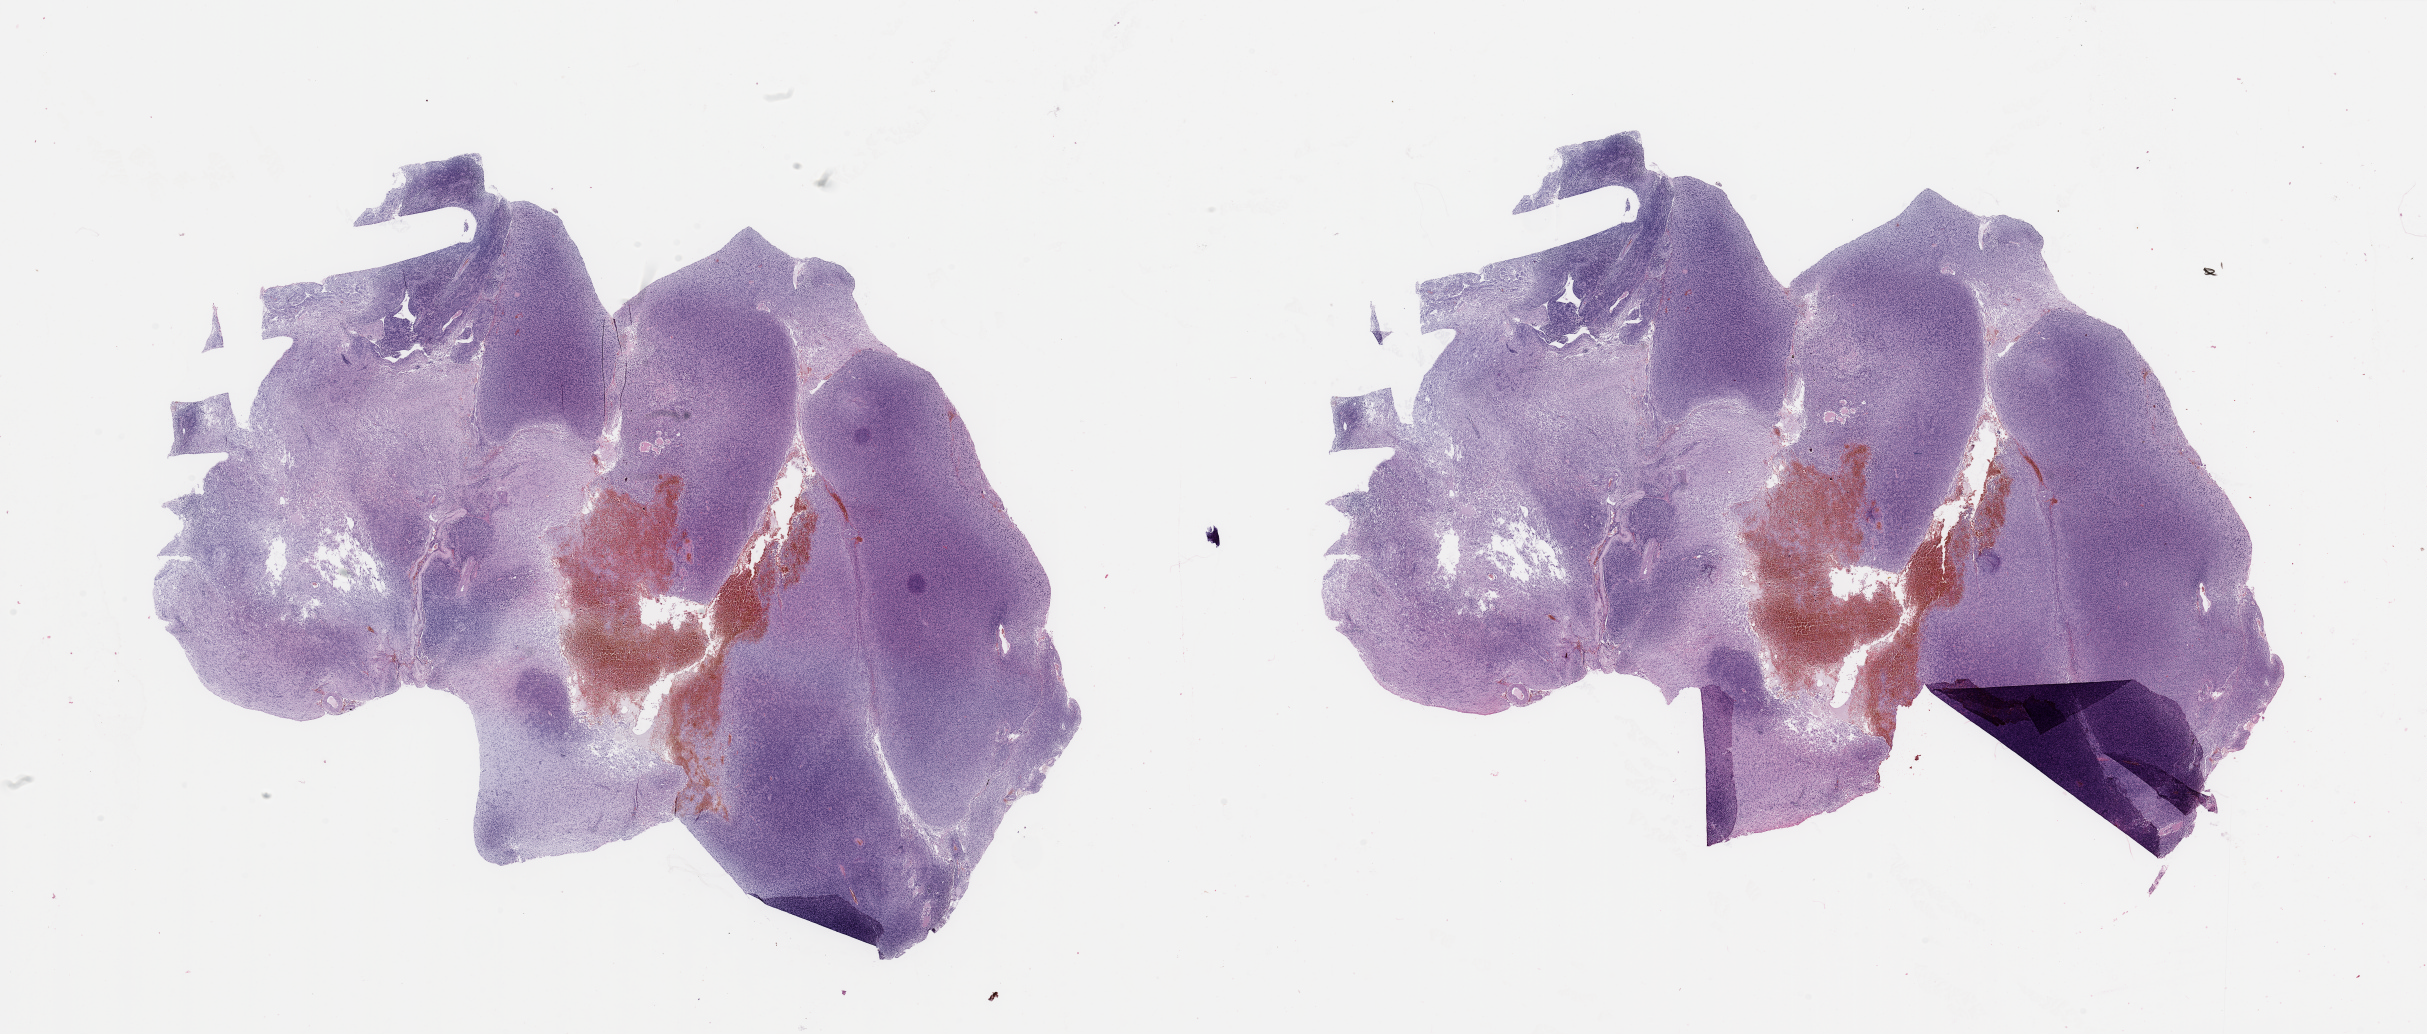
Digitized H&E tissue section (whole slide), whole scanned area (about 38.4 x 16.4 mm) shown as a low-resolution overview. Brain, tumour tissue. Male, 81 y/o.
Primary tumour site (as recorded): temporal lobe. Histologic diagnosis: Glioblastoma.